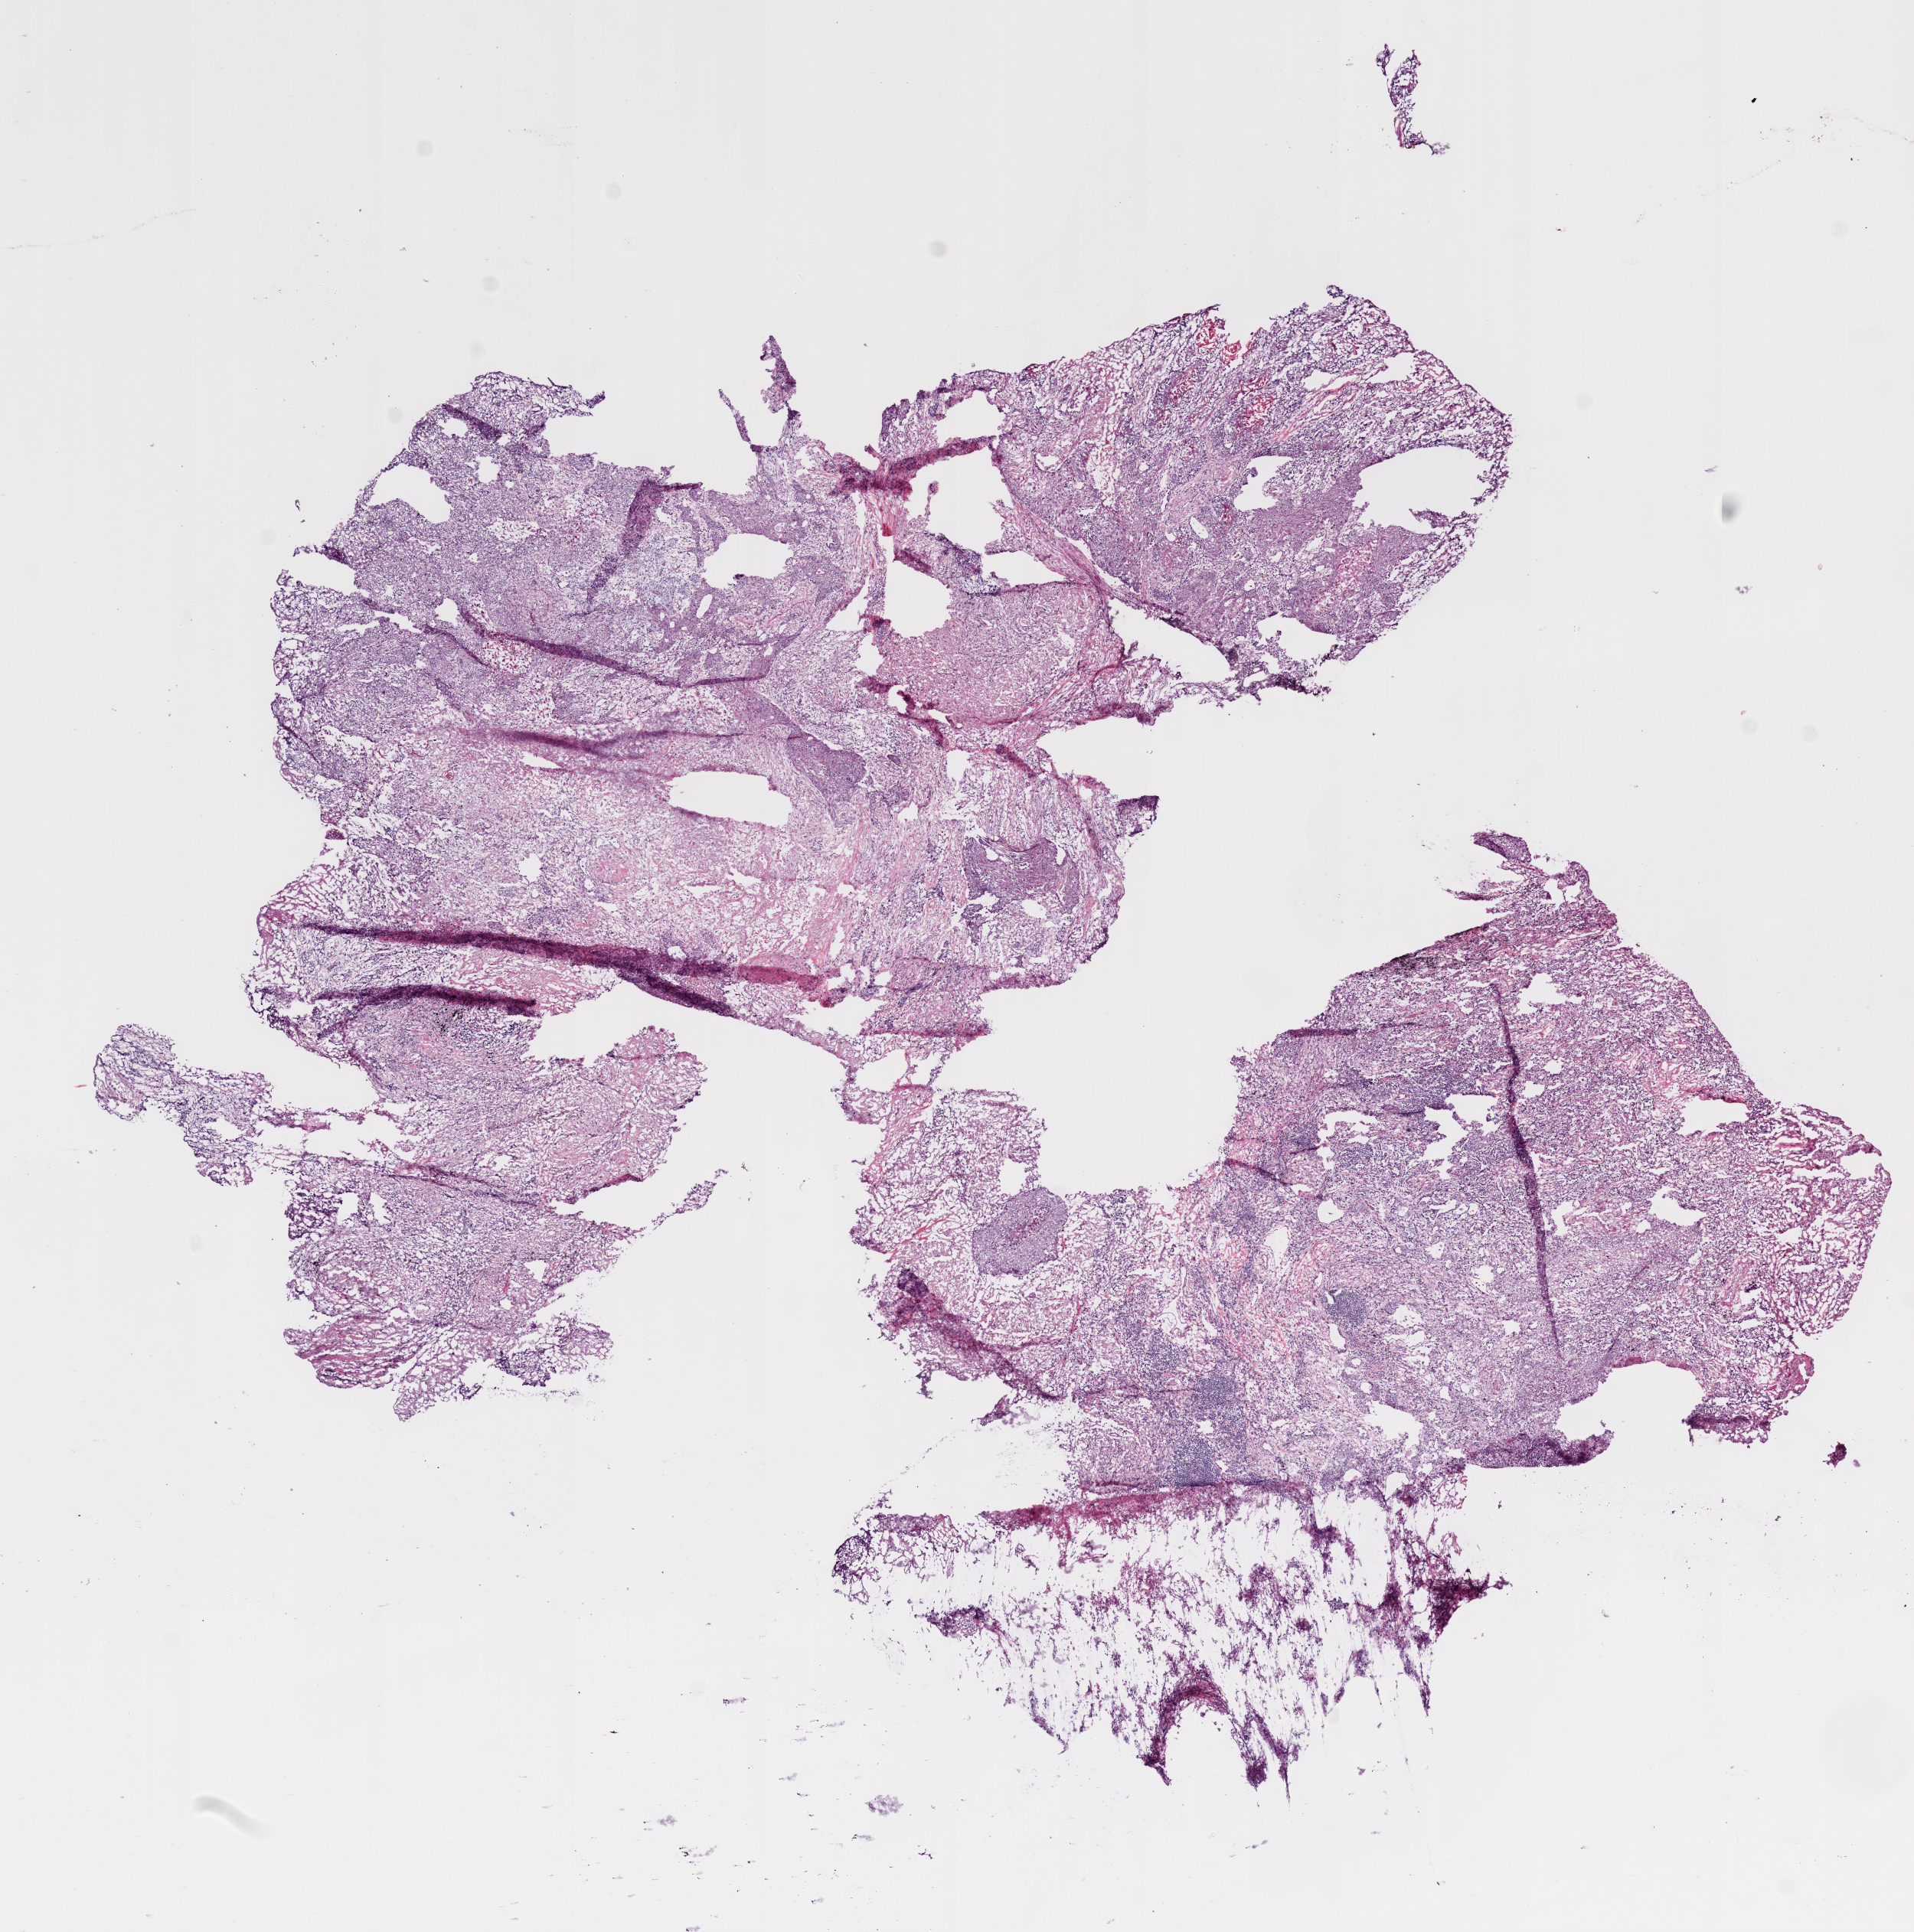
Digitized H&E-stained tissue section (whole slide) — shown as a low-resolution overview of the whole scanned area (about 10.0 x 10.1 mm, acquisition: 20x scan); frozen section from the bottom of the tissue portion; sample: primary tumour, lung. Patient: male, age at initial diagnosis 76 years. Slide review estimates, as recorded: tumour cells 70%, tumour nuclei 70%, normal cells 0%, stromal cells 25%, necrosis 5%.
• AJCC pathologic stage: IA
• pathologic diagnosis: Squamous cell carcinoma, NOS